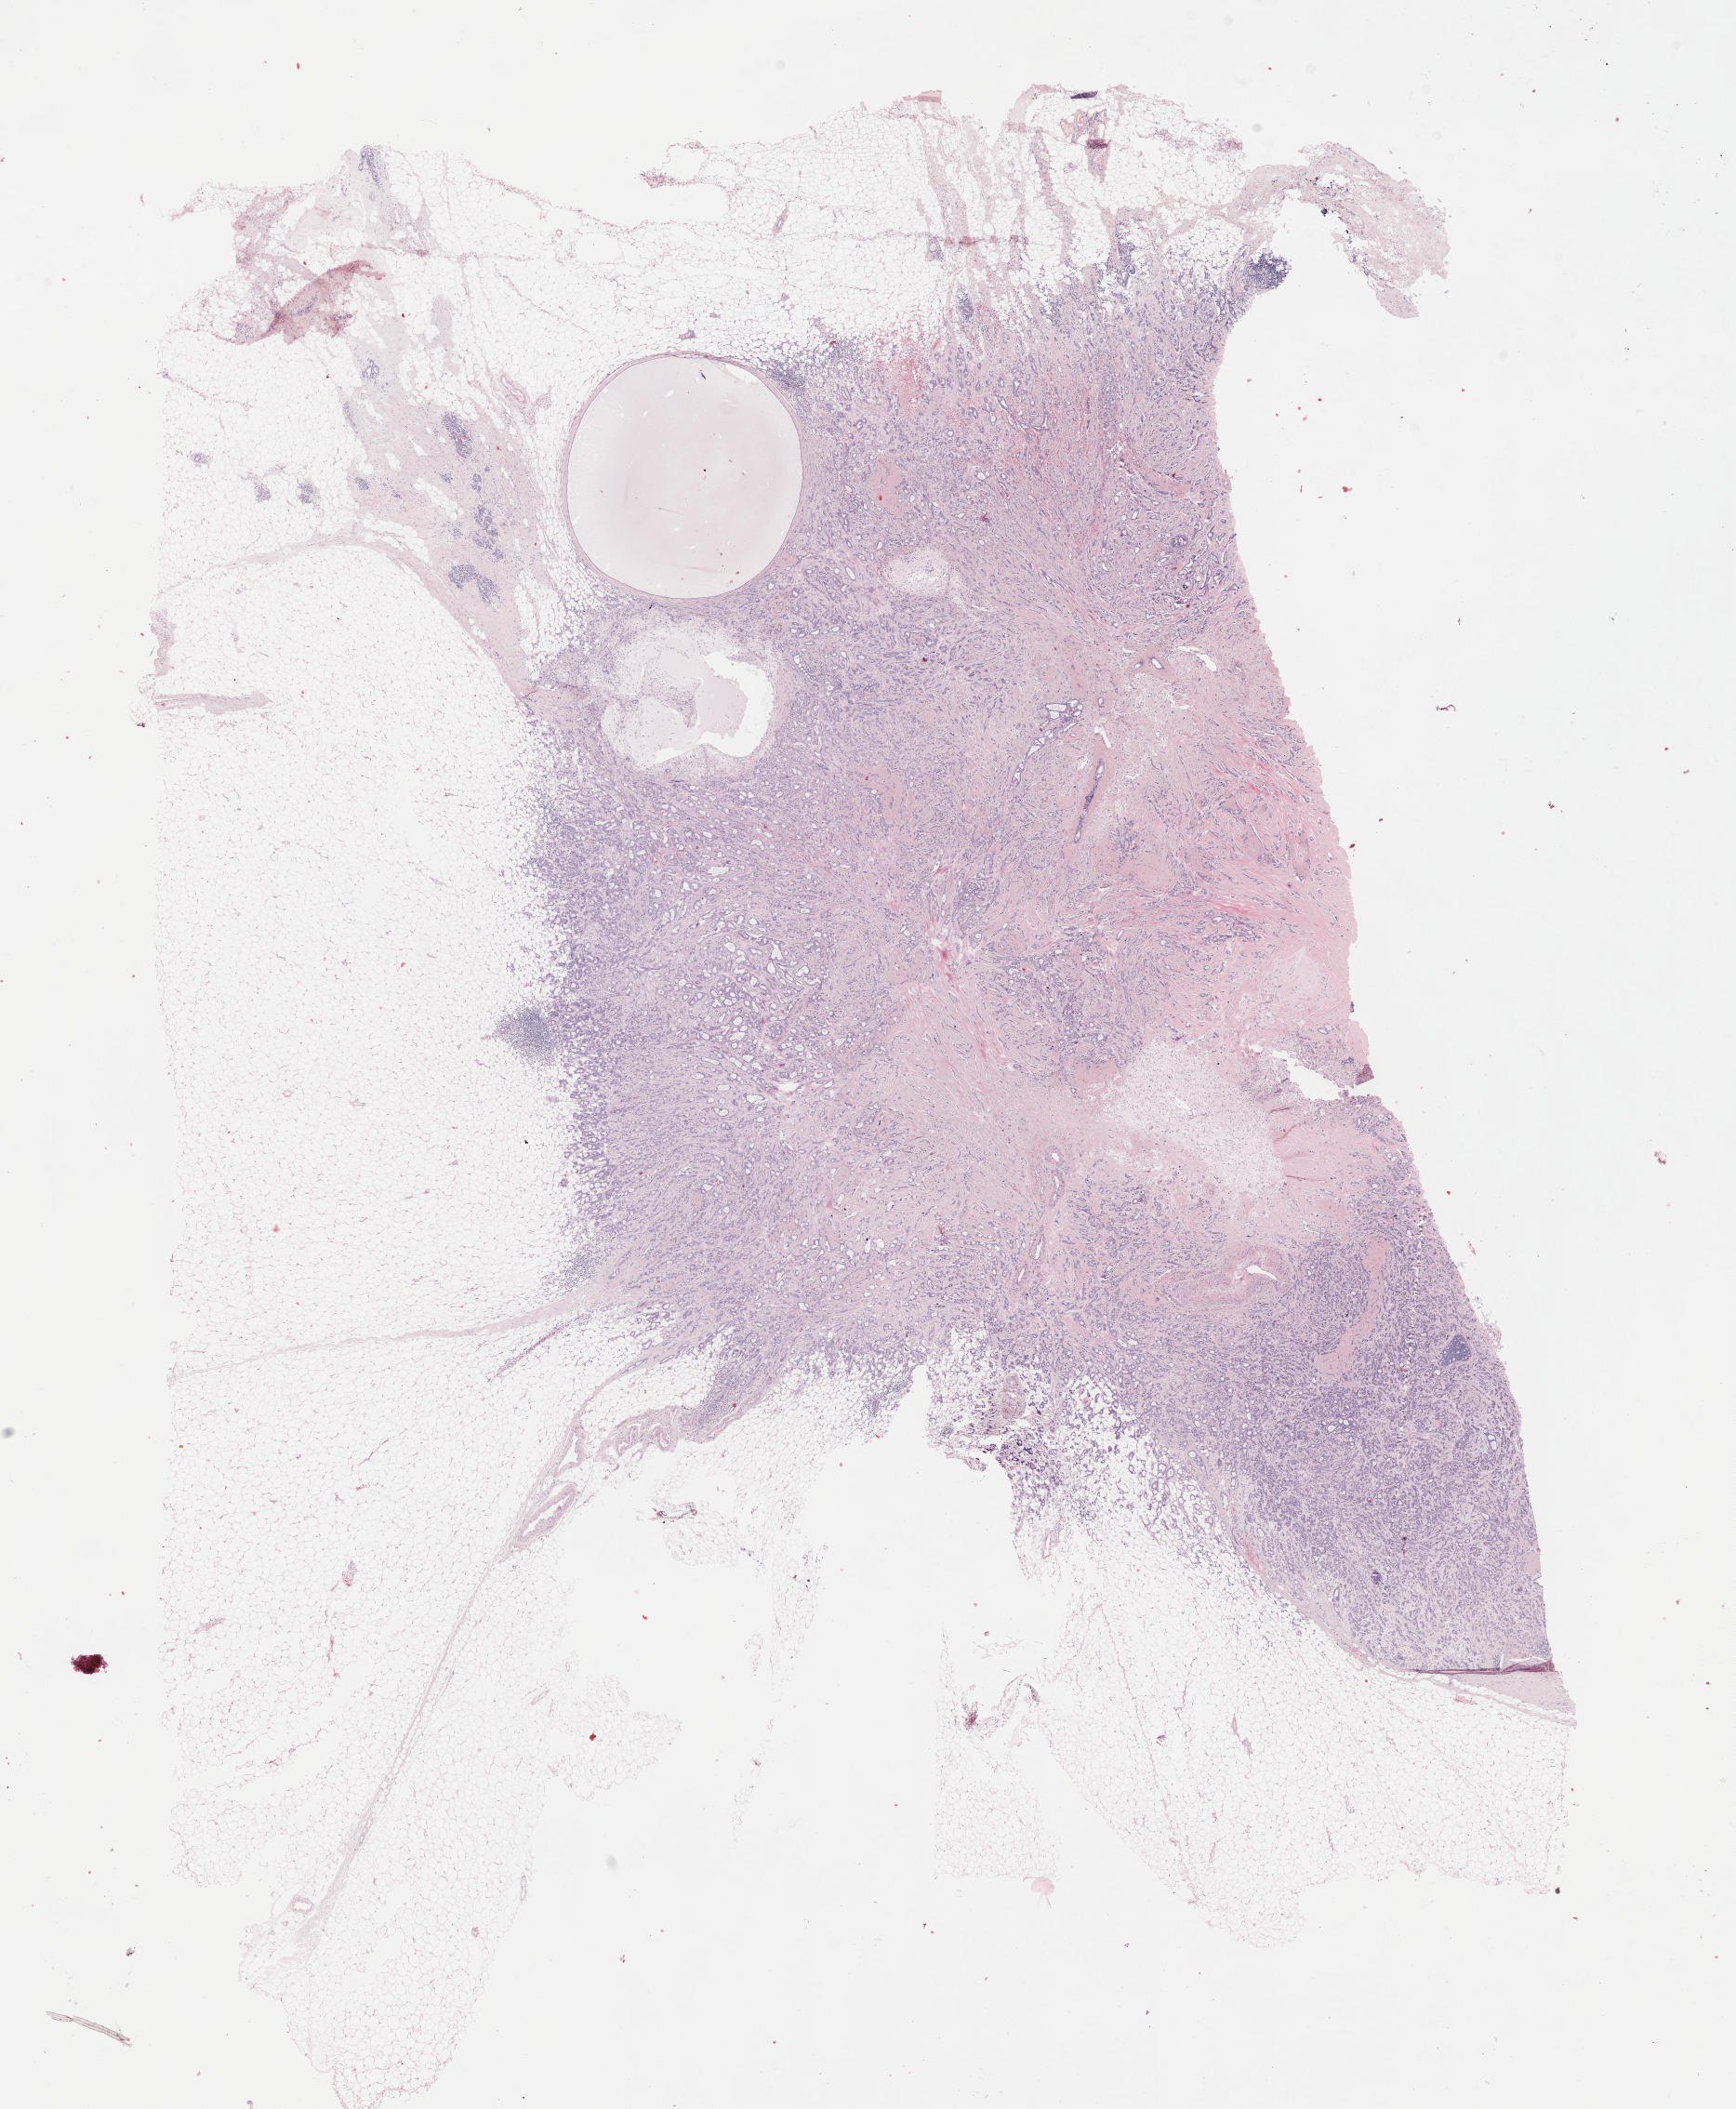
H&E whole-slide image — a low-resolution overview of the entire scanned area, about 15.1 x 18.3 mm (acquisition: 40x scan); FFPE section; breast, primary tumour sample. Female, age 53 years at initial diagnosis.
- laterality: left
- pathologic diagnosis: Tubular adenocarcinoma
- AJCC pathologic stage: IIA